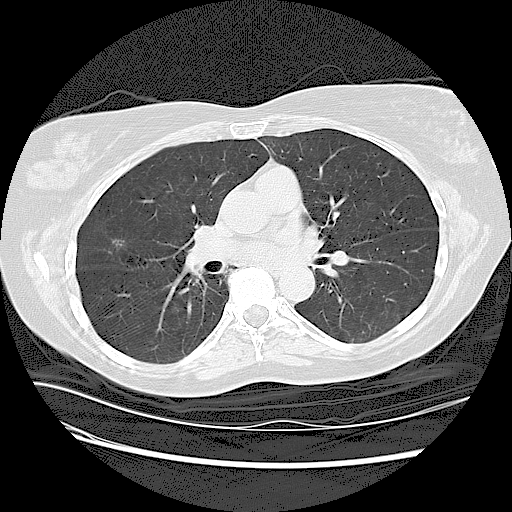
Low-dose screening chest CT, axial slice; baseline screening round; lung window (W 1500 / L -600 HU); lung (sharp) reconstruction kernel (LUNG). Female, age 63 years at enrolment. Current smoker at enrolment.
Lesion marked by an expert reader, box from (x=96, y=229) to (x=134, y=263) px. The exam's reader record, not a measurement of the box and not confirmed to be the same lesion: non-calcified nodule or mass ≥4 mm, right upper lobe, 7 × 7 mm, spiculated (stellate) margins, soft tissue attenuation. Participant outcome: lung cancer diagnosed 69 days after this screen — adenocarcinoma, NOS, right upper lobe, well differentiated (G1), stage IA (AJCC 6th edition), 90 mm at pathology.